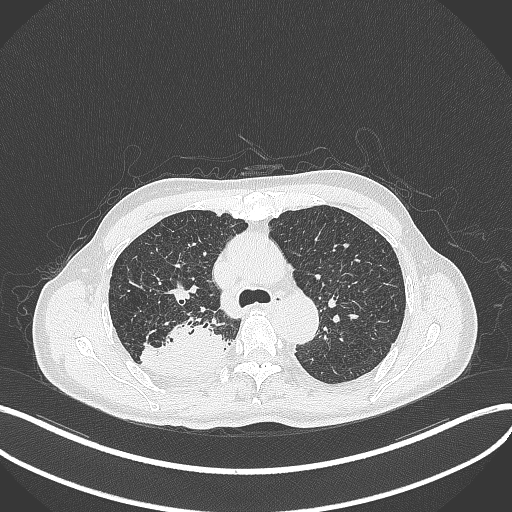
Chest CT, one axial slice. Lung window (W 1500 / L -600 HU). 1 mm slice thickness. 512 × 512 image matrix. Male patient, age 79 years. Case-level facts recorded for this patient, not image findings: clinical TNM (as recorded): T3 N0 M0.
Outlined on this slice (bounding box drawn by a radiologist):
- lung tumour (recorded histology: adenocarcinoma): bounding box <139,316,228,382> (left, top, right, bottom; pixels)